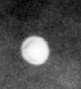
Cropped region of a digitized screen-film mammogram centred on a radiologist-marked abnormality; right breast; CC view; BI-RADS breast density category 3 (scale 1–4).
Calcifications, morphology round and regular / lucent center; BI-RADS assessment category 2; benign without callback (not worked up further).